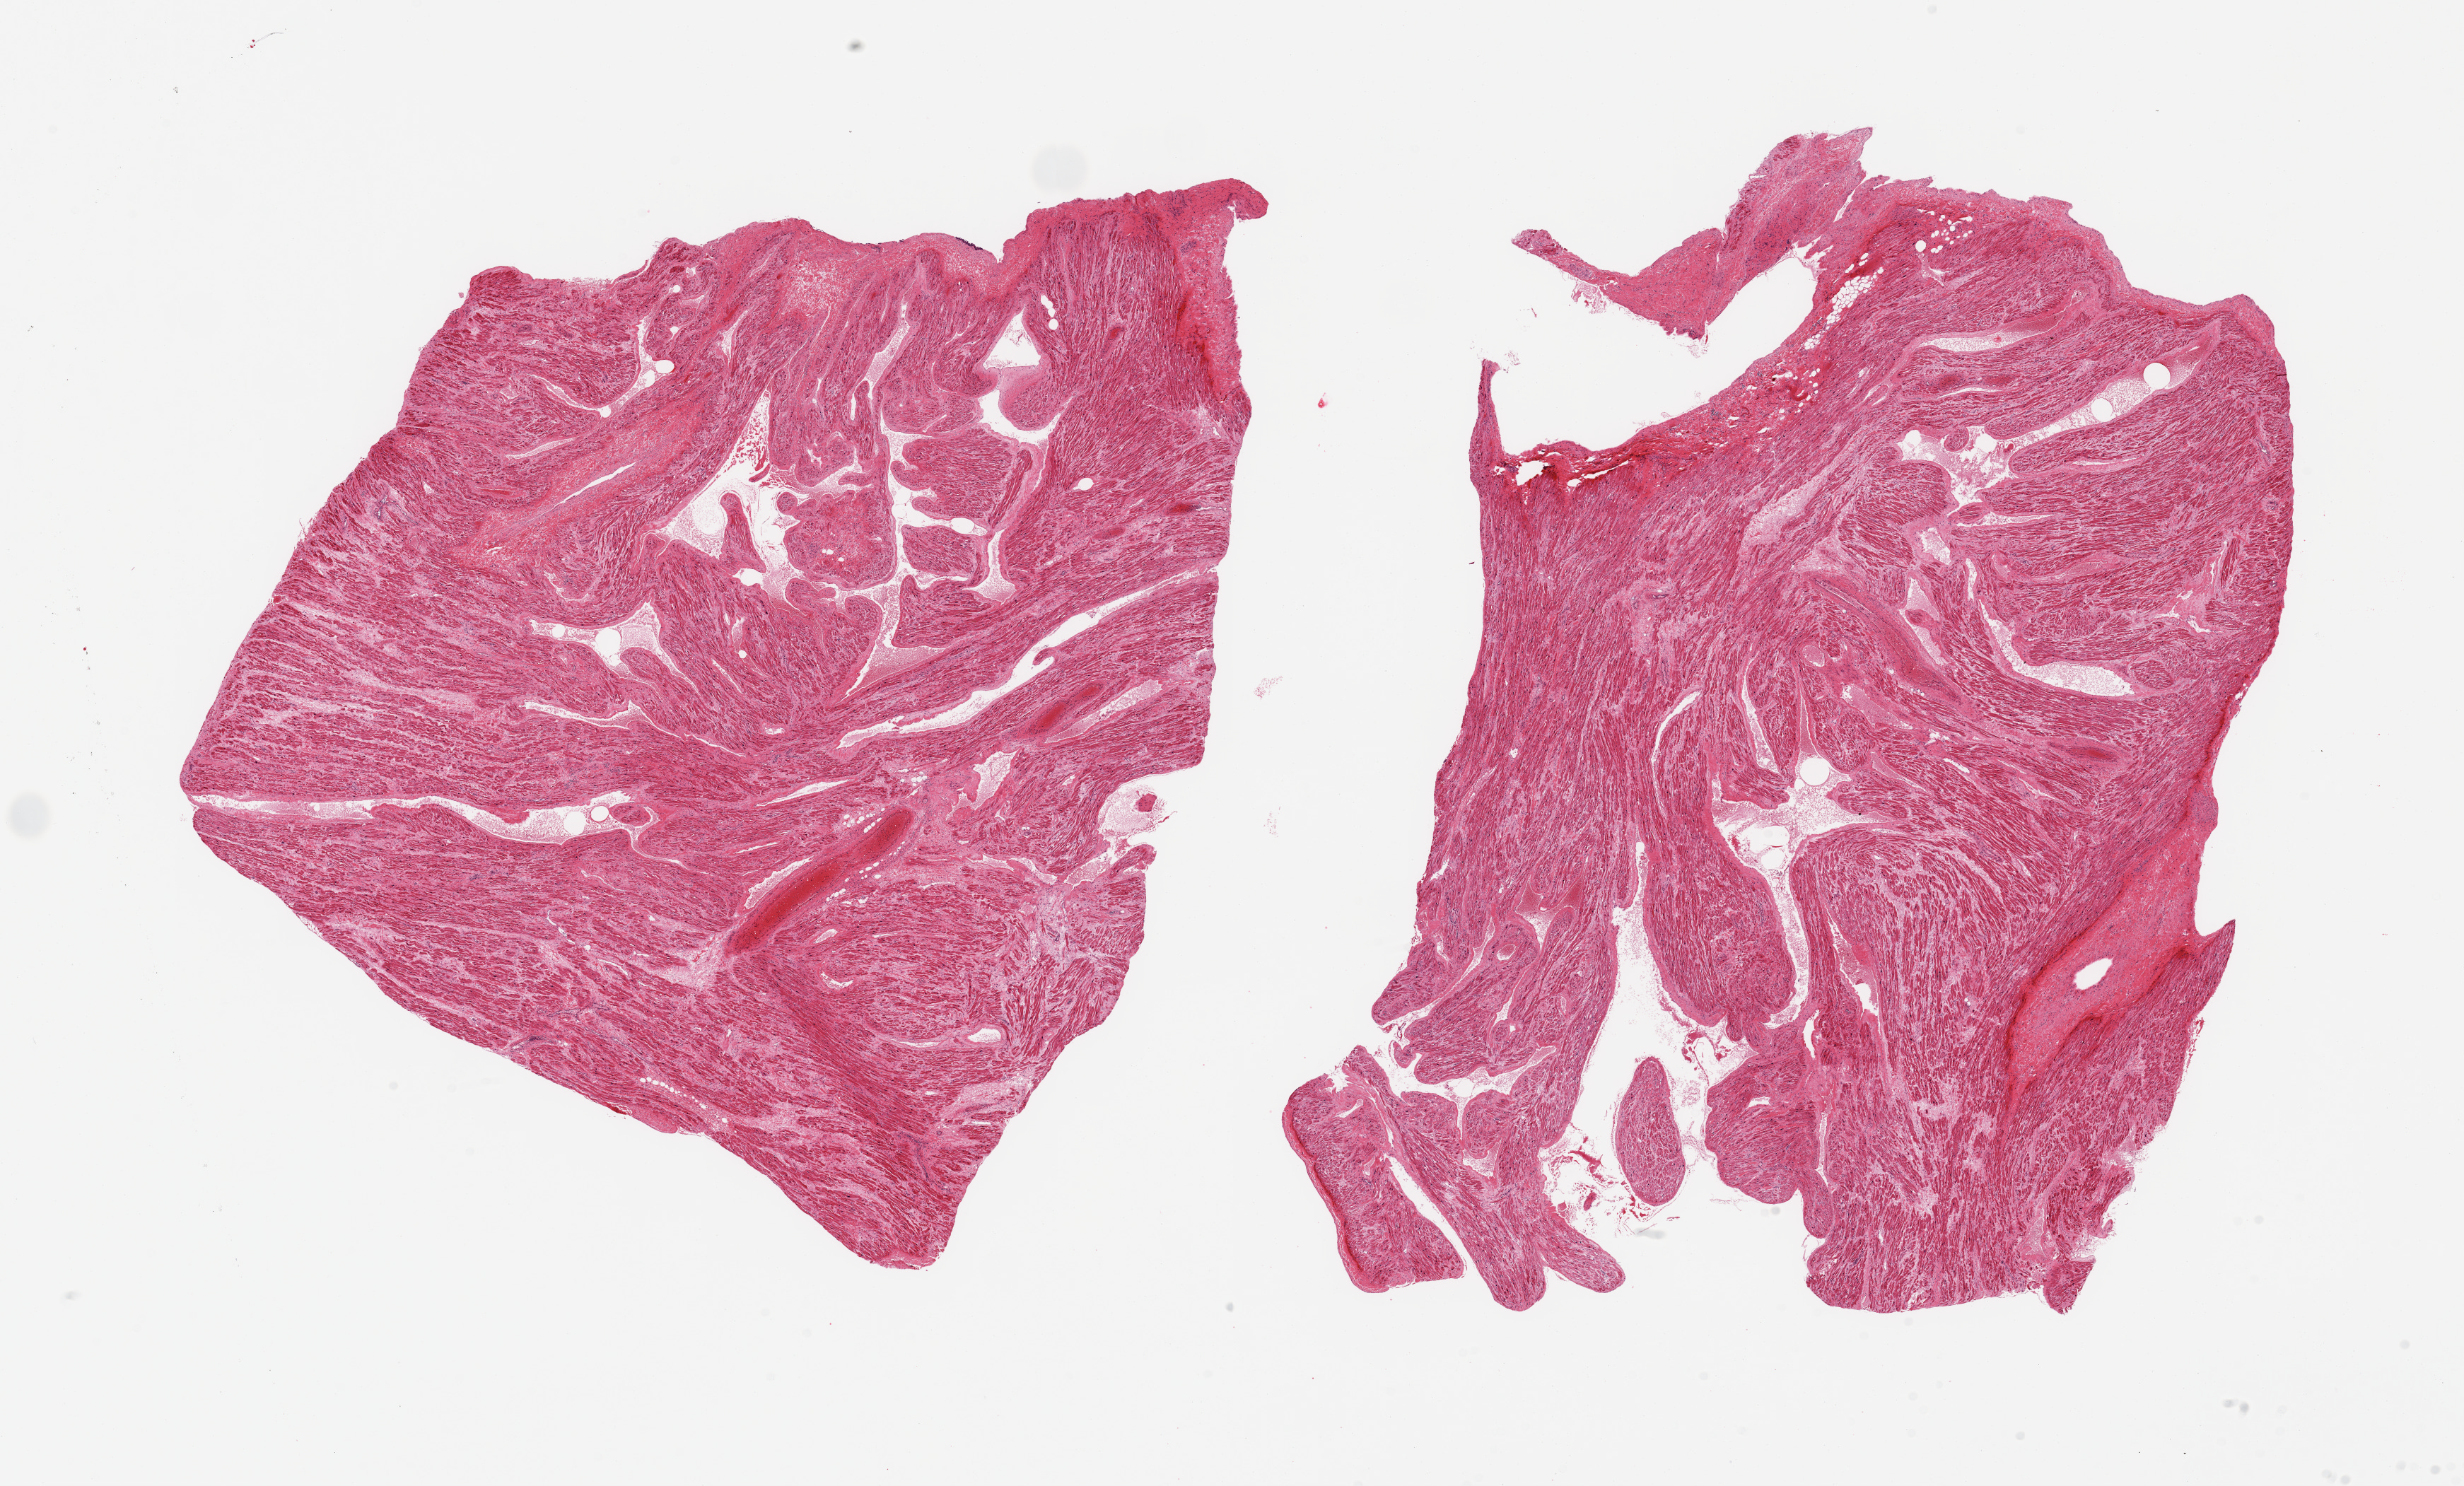
Whole-slide image, hematoxylin and eosin (H&E) stain, a low-resolution overview of the entire scanned area, about 27.6 x 16.6 mm (from a 20x scan); PAXgene-fixed paraffin-embedded (PFPE) section; section of auricular appendage (target tissue); tissue donor sample. Donor: male.
- reviewer comment on this tissue sample: 2 pieces, no abnormalities